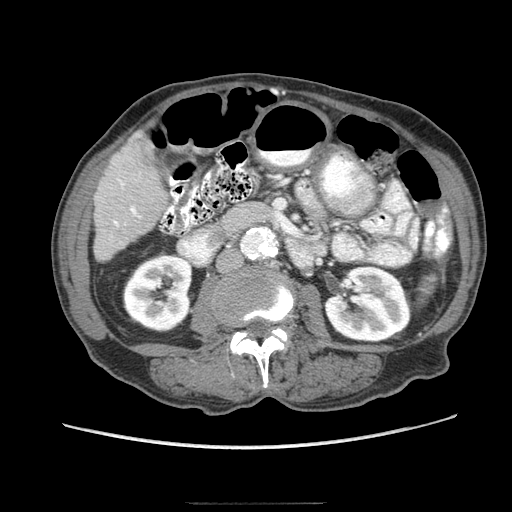
Contrast-enhanced abdominal CT (liver protocol), one axial slice. Slice 23 of 83 in the series (ordered by position). Reconstruction kernel STANDARD. 140 kVp. Soft-tissue window (W 400 / L 40 HU). 512 × 512 image matrix, field of view 360 × 360 mm. Case-level facts recorded for this patient, not image findings: diagnosis: hepatocellular carcinoma (patient treated with transarterial chemoembolisation; whether this scan precedes or follows treatment is not stated here); TNM stage (as recorded): Stage-I; Child-Pugh class: A; tumour differentiation: moderately differentiated.
Annotated regions visible in this slice (semi-automatically segmented with operator editing):
- liver parenchyma outside the tumour (the mass and vessels are separate outlines, so this box may not span the whole liver): bounding box <94,132,166,260> (left, top, right, bottom; pixels)
- liver vessels: <113,179,140,226>